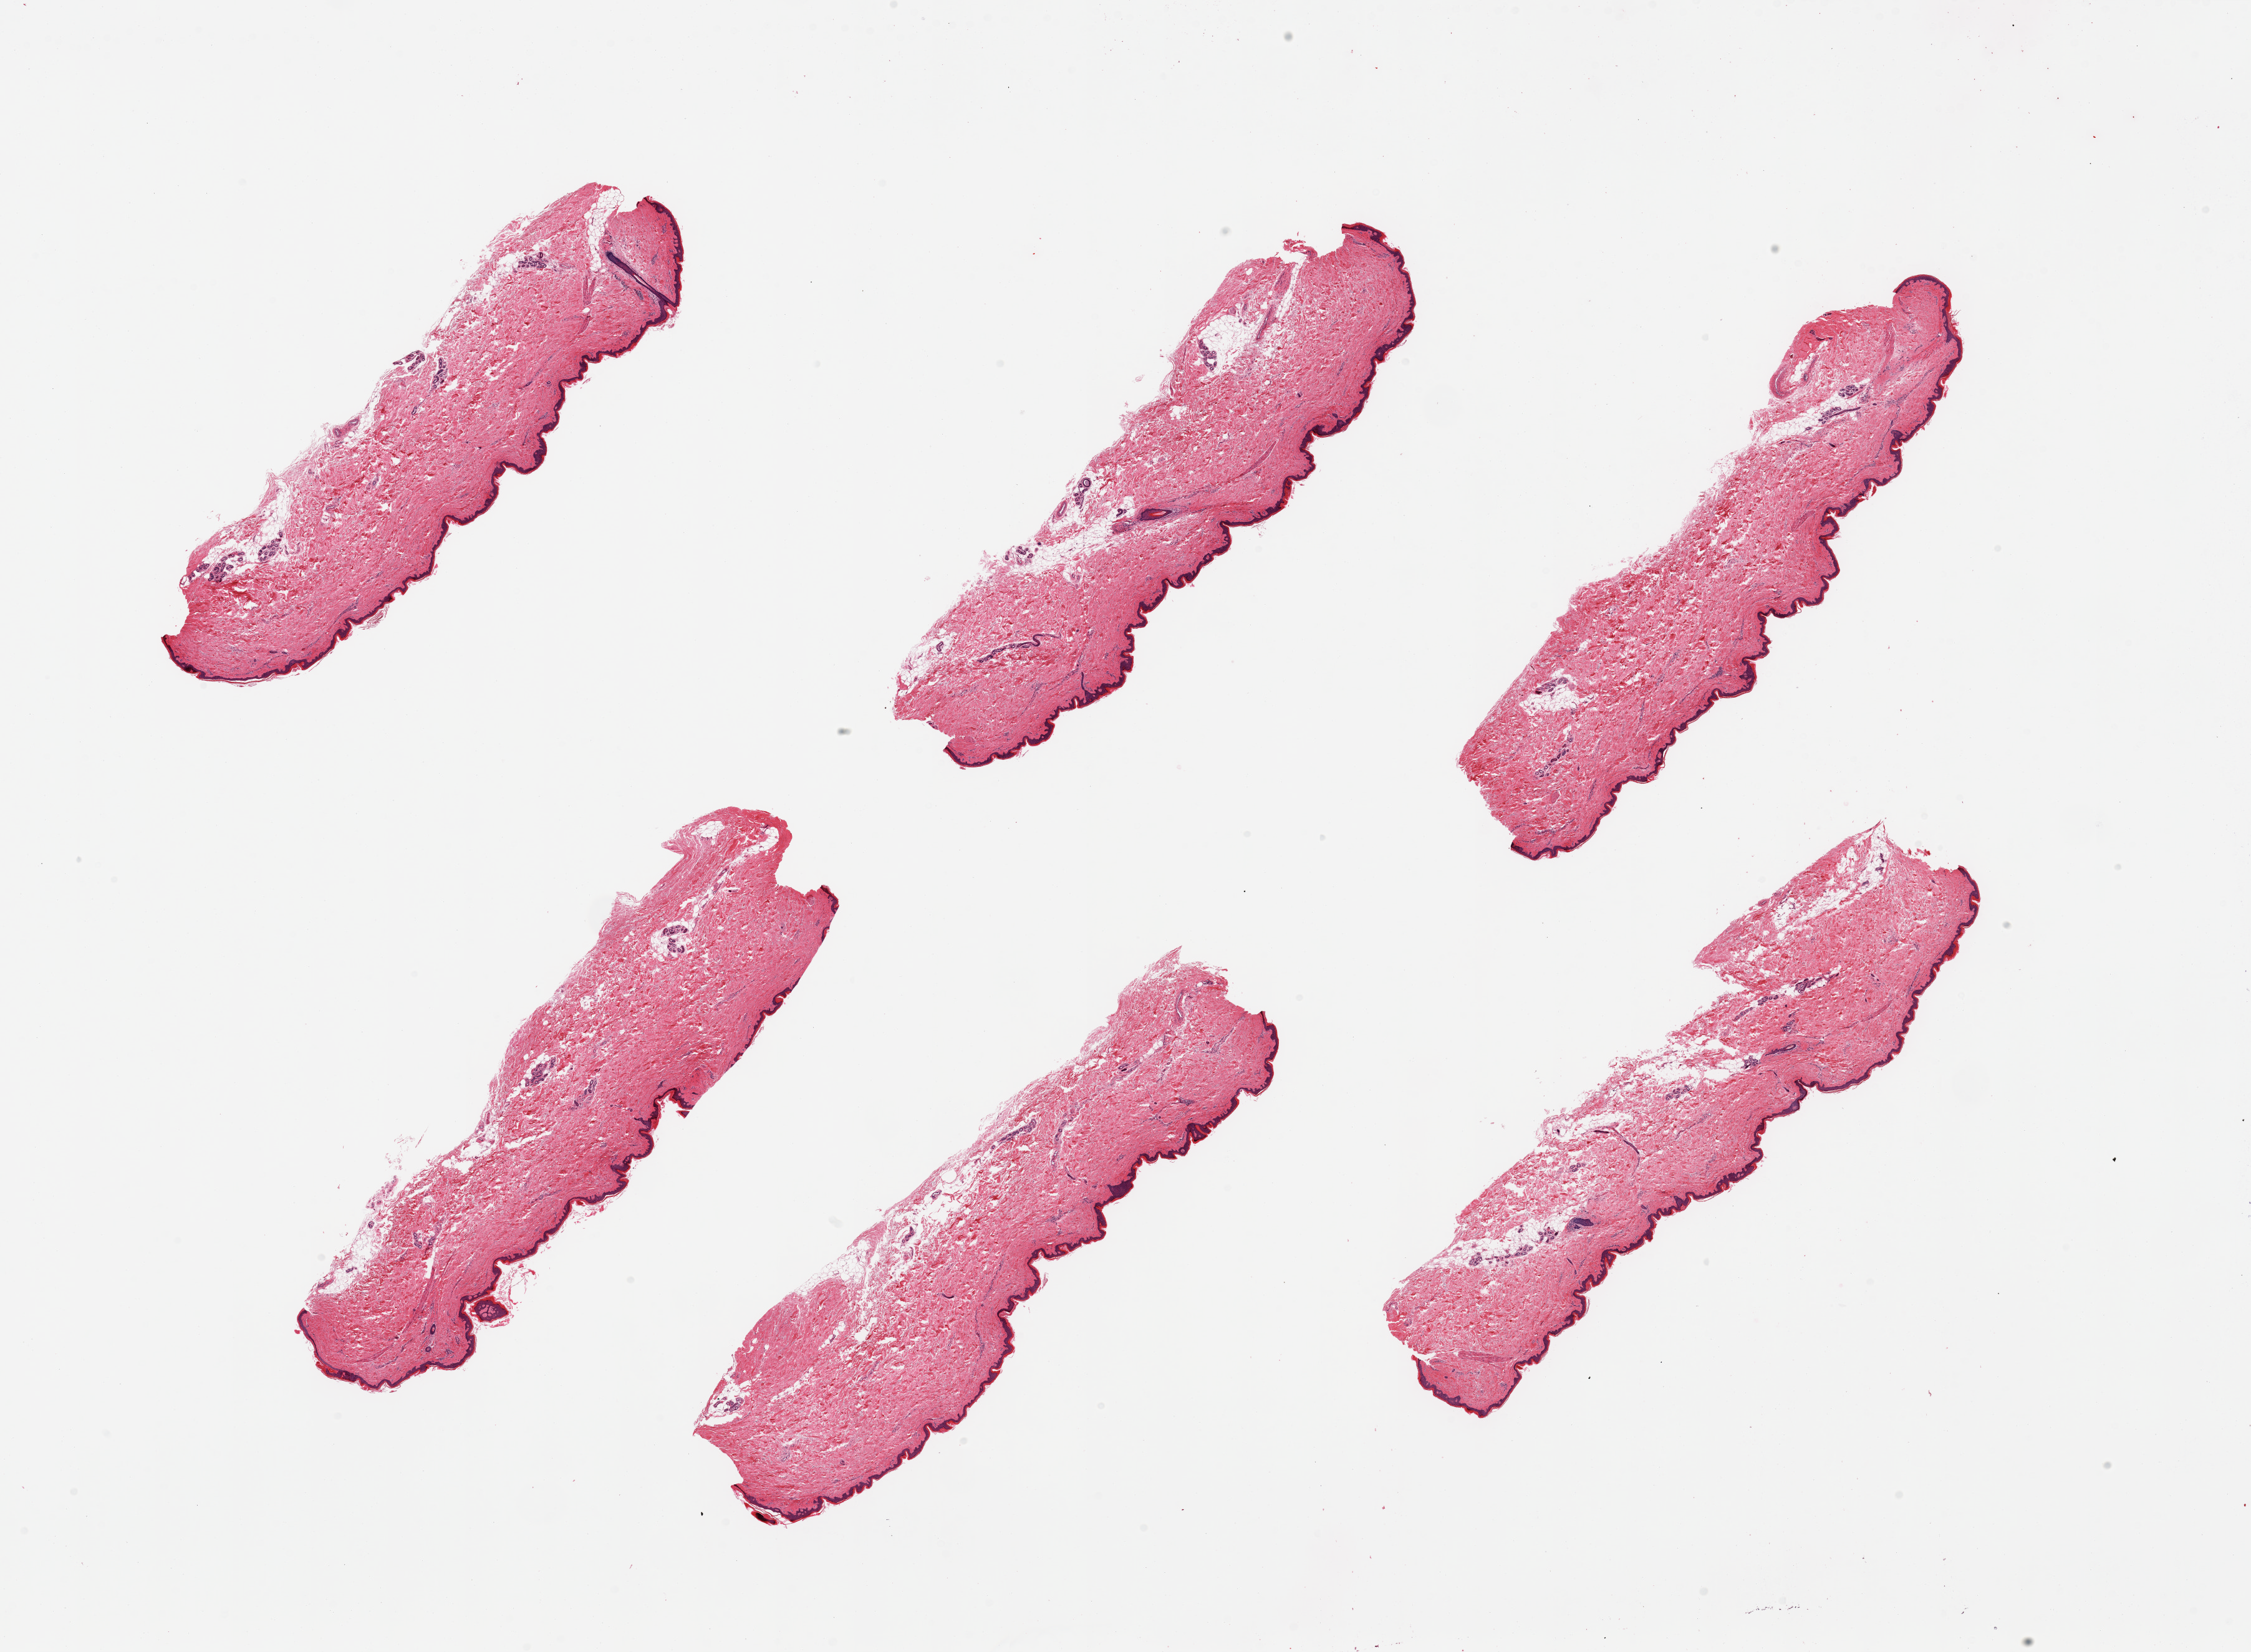
Hematoxylin and eosin (H&E) whole-slide image, a low-resolution overview of the entire scanned area, about 28.5 x 21.0 mm, PAXgene-fixed, paraffin-embedded tissue, sampled site (target tissue): skin of lower leg, tissue donor sample. Female donor.
* review note (as recorded): 6 pieces; well trimmed, epidermis measures 32 microns, small amount of internal fat